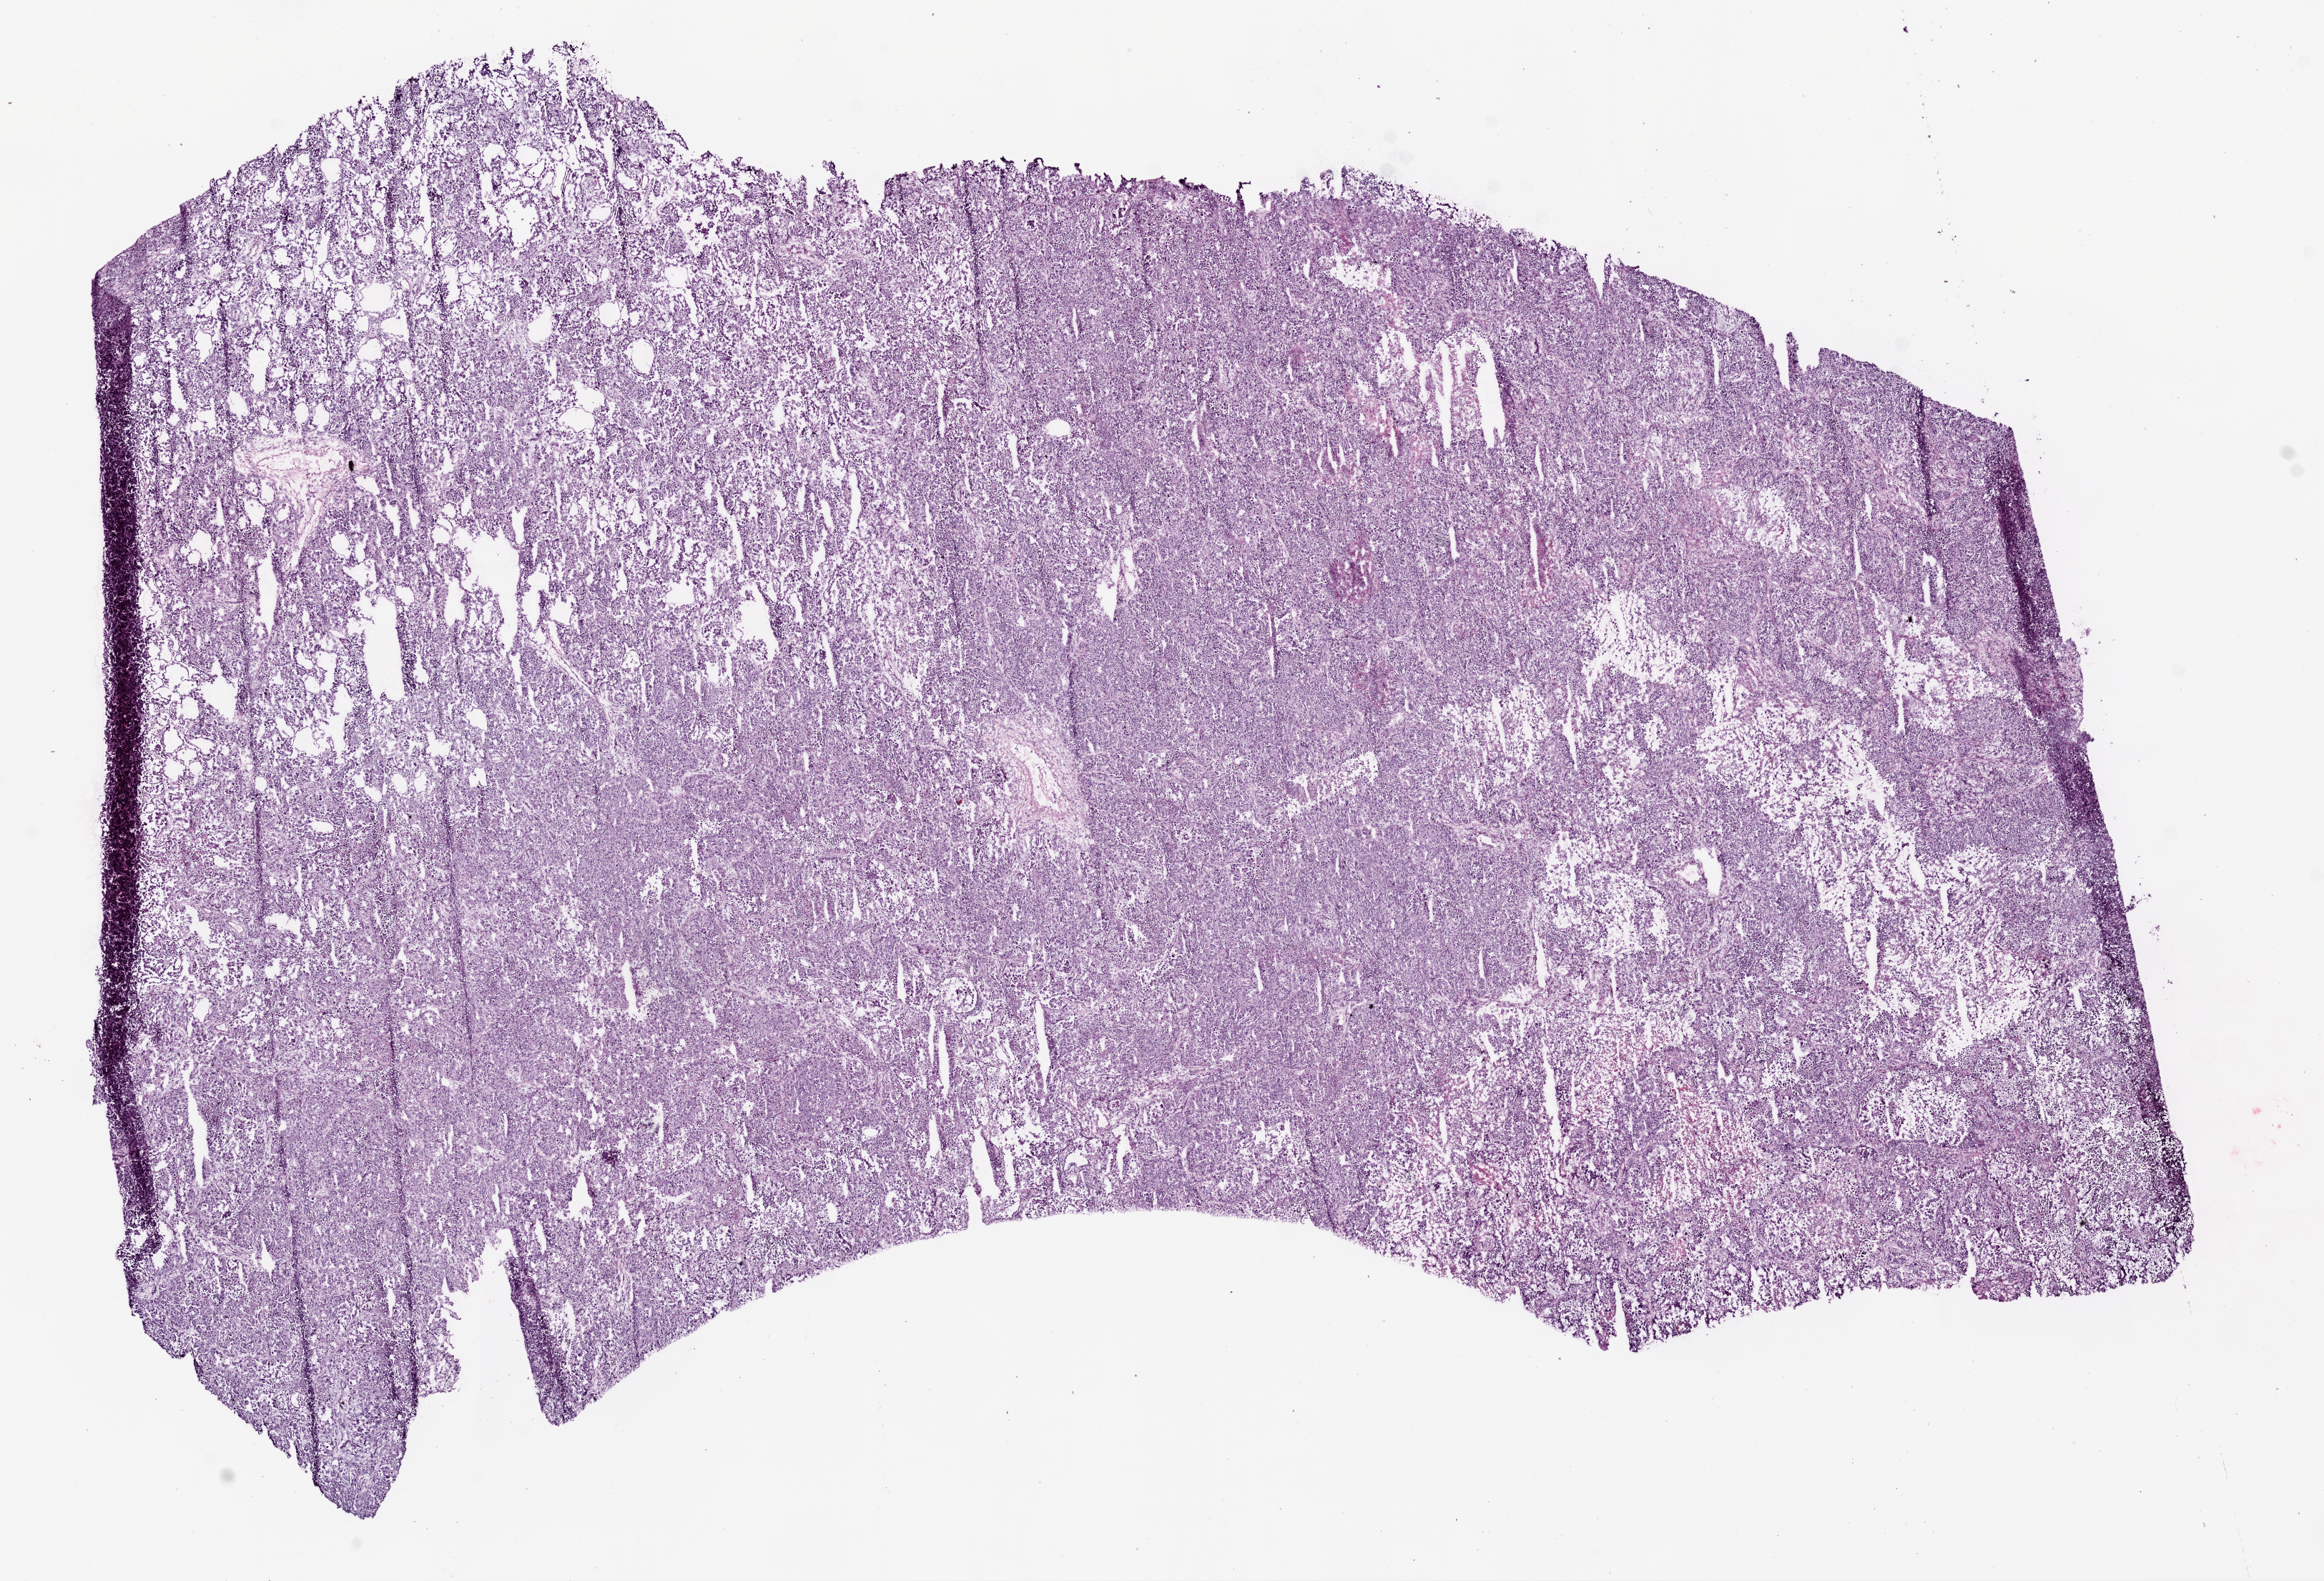
Whole-slide histology image, Hematoxylin and eosin (H&E) stained — whole scanned area (about 13.0 x 8.9 mm, from a 20x scan) shown as a low-resolution overview. Frozen section. Primary tumour sample from the lung. Male patient; age at initial diagnosis 71 years. Slide review estimates, as recorded: tumour cells 88%, tumour nuclei 75%, normal cells 0%, stromal cells 10%, necrosis 2%.
* diagnosis: Adenocarcinoma with mixed subtypes (lower lobe, lung)
* TNM: T2 N0 M0
* laterality: left
* AJCC pathologic stage: IB (6th edition)